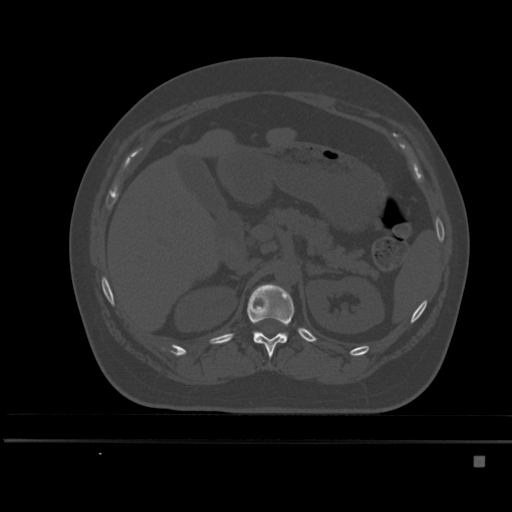
CT including the spine, one axial slice. Slice 211 of 495 in the series (ordered by position). Bone window (W 1800 / L 400 HU). 1.5 mm slice thickness. 512 × 512 image matrix, field of view 404 × 404 mm. Patient: female, 33 years. Case-level facts recorded for this patient, not image findings: primary cancer: breast.
Structures marked on this image (semi-automatic segmentation, software-assisted and operator-edited):
- T12 vertebra: bounding box <247,284,294,358> (left, top, right, bottom; pixels)